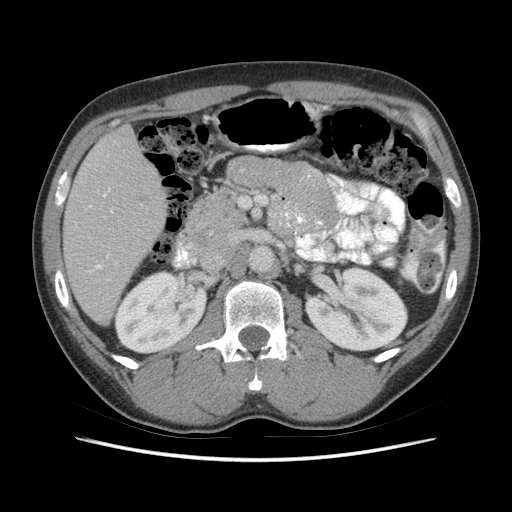
Contrast-enhanced abdominal CT (liver protocol), one axial slice. Position 25 of 73 along the scan axis. Reconstruction kernel STANDARD. Soft-tissue window (W 400 / L 40 HU). 2.5 mm slice thickness. 512 × 512 image matrix, field of view 360 × 360 mm. Case-level facts recorded for this patient, not image findings: diagnosis: hepatocellular carcinoma (patient treated with transarterial chemoembolisation; whether this scan precedes or follows treatment is not stated here); TNM stage (as recorded): Stage-IIIA; Child-Pugh class: A; tumour nodularity: multinodular; tumour size: 6.6 cm.
Annotated regions visible in this slice (semi-automatic segmentation, software-assisted and operator-edited):
- liver parenchyma outside the tumour (the mass and vessels are separate outlines, so this box may not span the whole liver): bounding box [x1, y1, x2, y2] px = [62, 126, 166, 324]
- liver vessels: [89, 188, 113, 268]